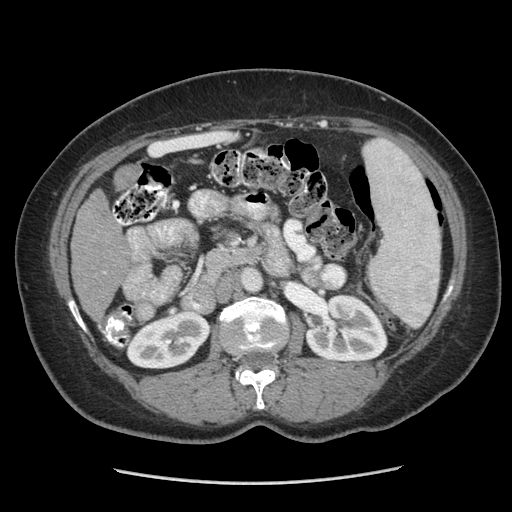
Contrast-enhanced abdominal CT (liver protocol), one axial slice. Slice 126 of 185 in the series (ordered by position). Reconstruction kernel STANDARD. Soft-tissue window (W 400 / L 40 HU). 2.5 mm slice thickness. 512 × 512 image matrix, field of view 360 × 360 mm. From the clinical record (not read from this slice): diagnosis: hepatocellular carcinoma (patient treated with transarterial chemoembolisation; whether this scan precedes or follows treatment is not stated here); TNM stage (as recorded): Stage-I; Child-Pugh class: A; tumour differentiation: poorly differentiated.
Outlined on this slice (semi-automatic segmentation, software-assisted and operator-edited):
- liver parenchyma outside the tumour (the mass and vessels are separate outlines, so this box may not span the whole liver): bounding box <70,190,128,314> (left, top, right, bottom; pixels)
- mass: <114,164,141,190>